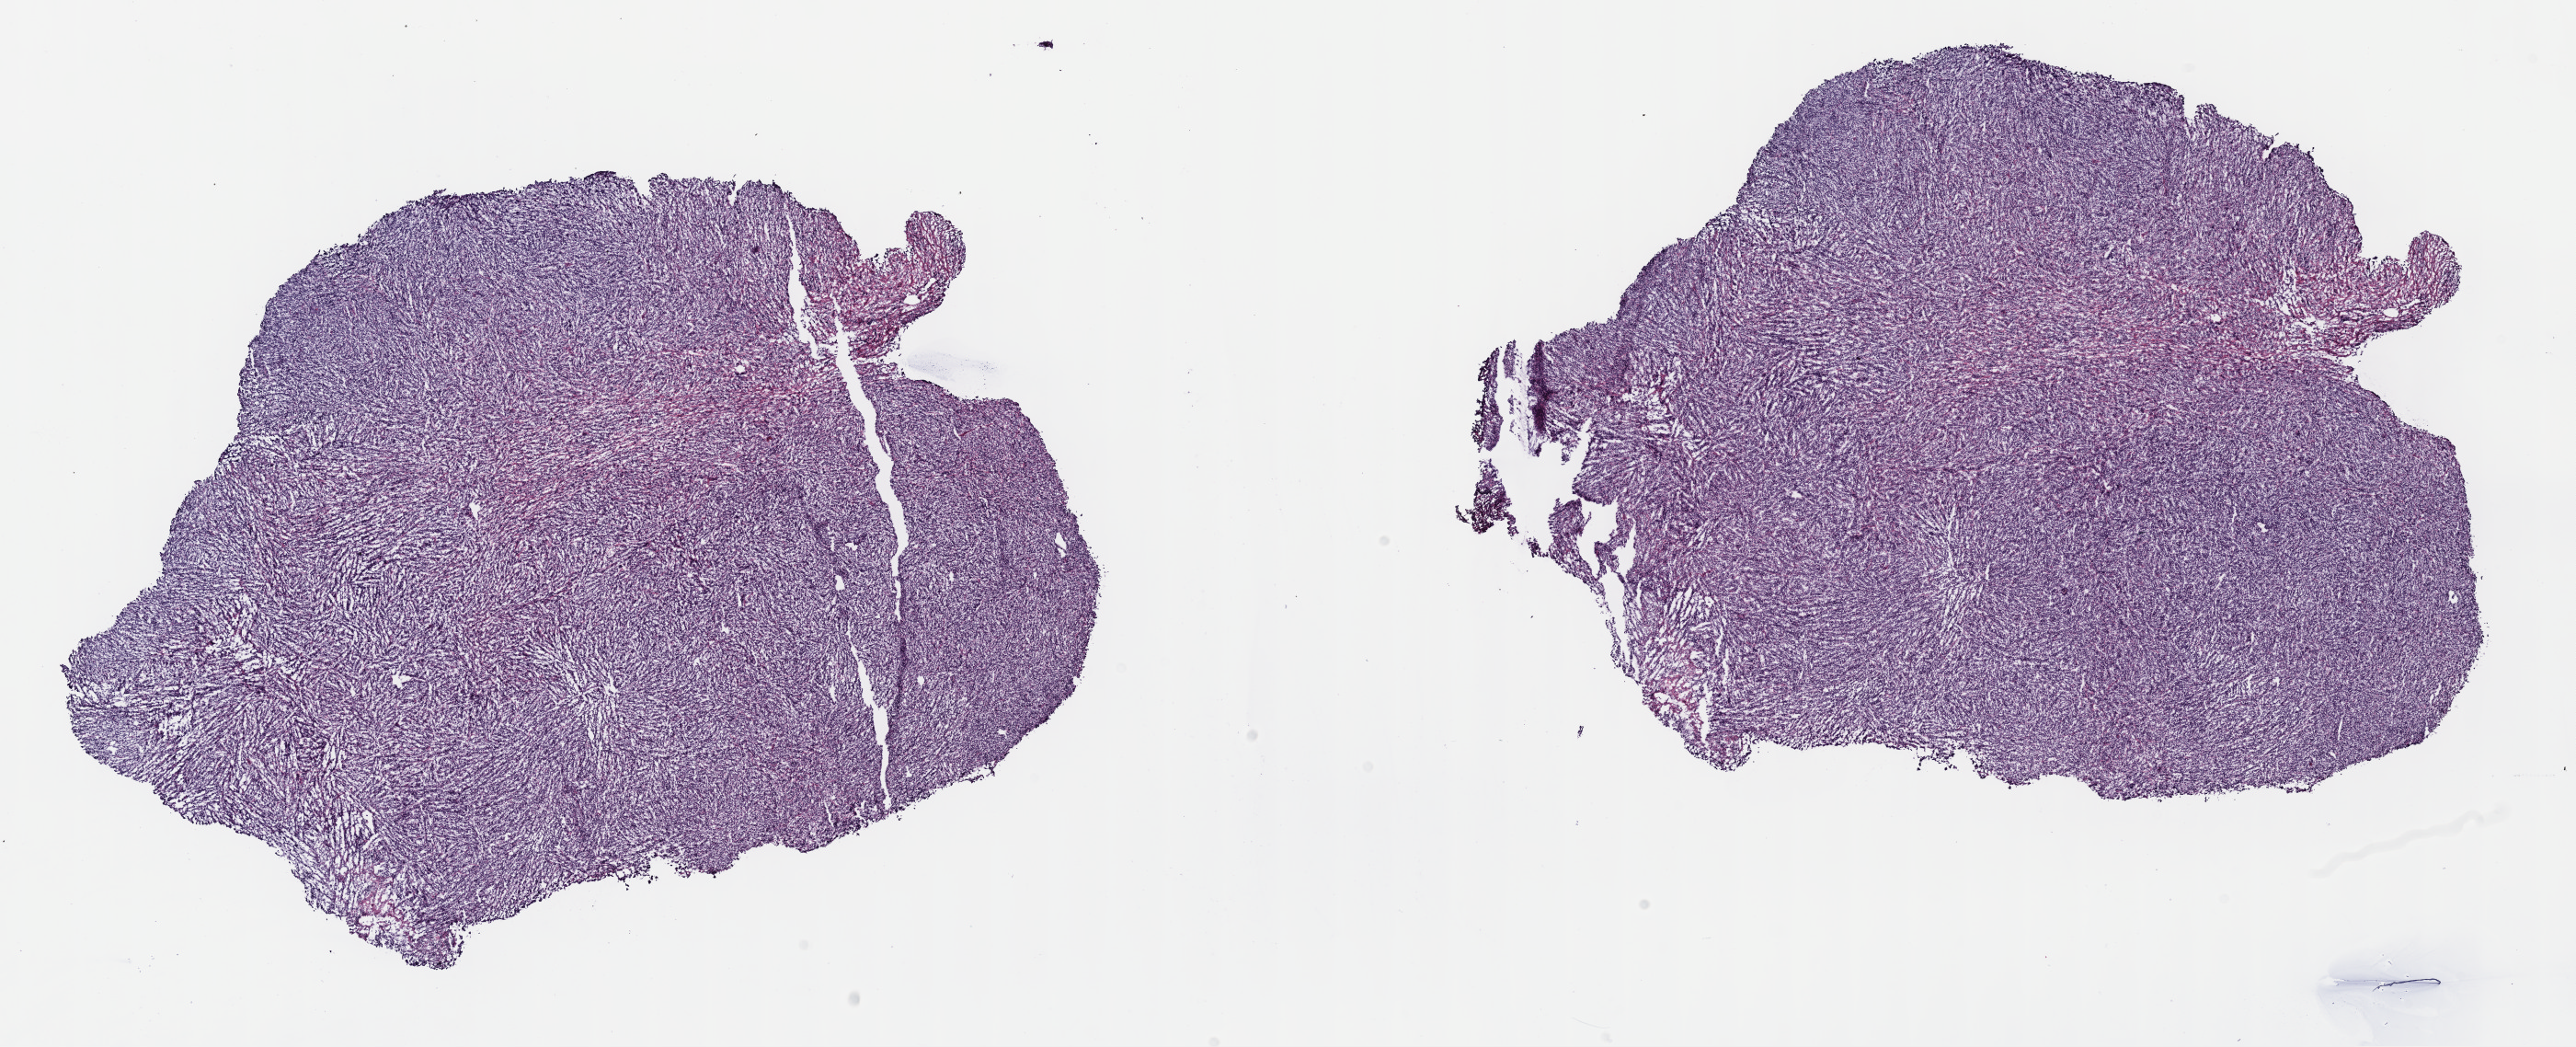
Digitized Hematoxylin and eosin (H&E) stained tissue section (whole slide) — low-resolution overview of the scanned area, about 22.7 x 9.2 mm, frozen section from the top of the tissue portion, primary tumour sample from the lymphoid tissue. Female, age 69 years at initial diagnosis. Pathologist review of this section (percent, as recorded): tumour cells 90%, tumour nuclei 90%, normal cells 5%, stromal cells 5%, necrosis 0%. Infiltration values recorded for this section: lymphocyte infiltration 60%, monocyte infiltration 20%, neutrophil infiltration 10%.
Diagnosis: Diffuse large B-cell lymphoma, NOS.